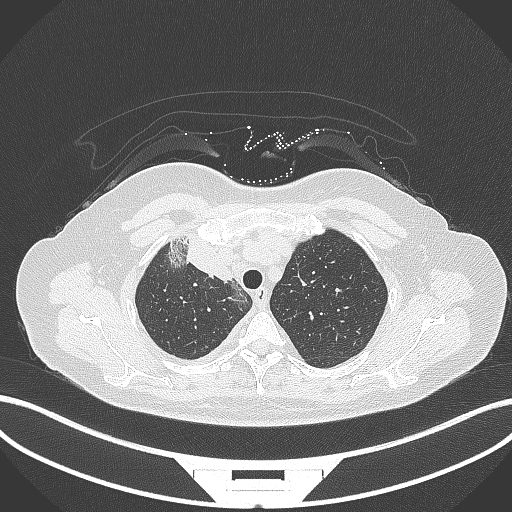
Chest CT, one axial slice; position 249 of 305 along the scan axis; reconstruction kernel B70f; lung window (W 1500 / L -600 HU); 512 × 512 image matrix, field of view 400 × 400 mm. Patient: female, 52 years. From the clinical record (not read from this slice): clinical TNM (as recorded): T3 N1 M1.
Outlined on this slice (rectangle marked by the reading radiologist):
- lung tumour (recorded histology: adenocarcinoma): bounding box [x1, y1, x2, y2] px = [165, 229, 235, 285]